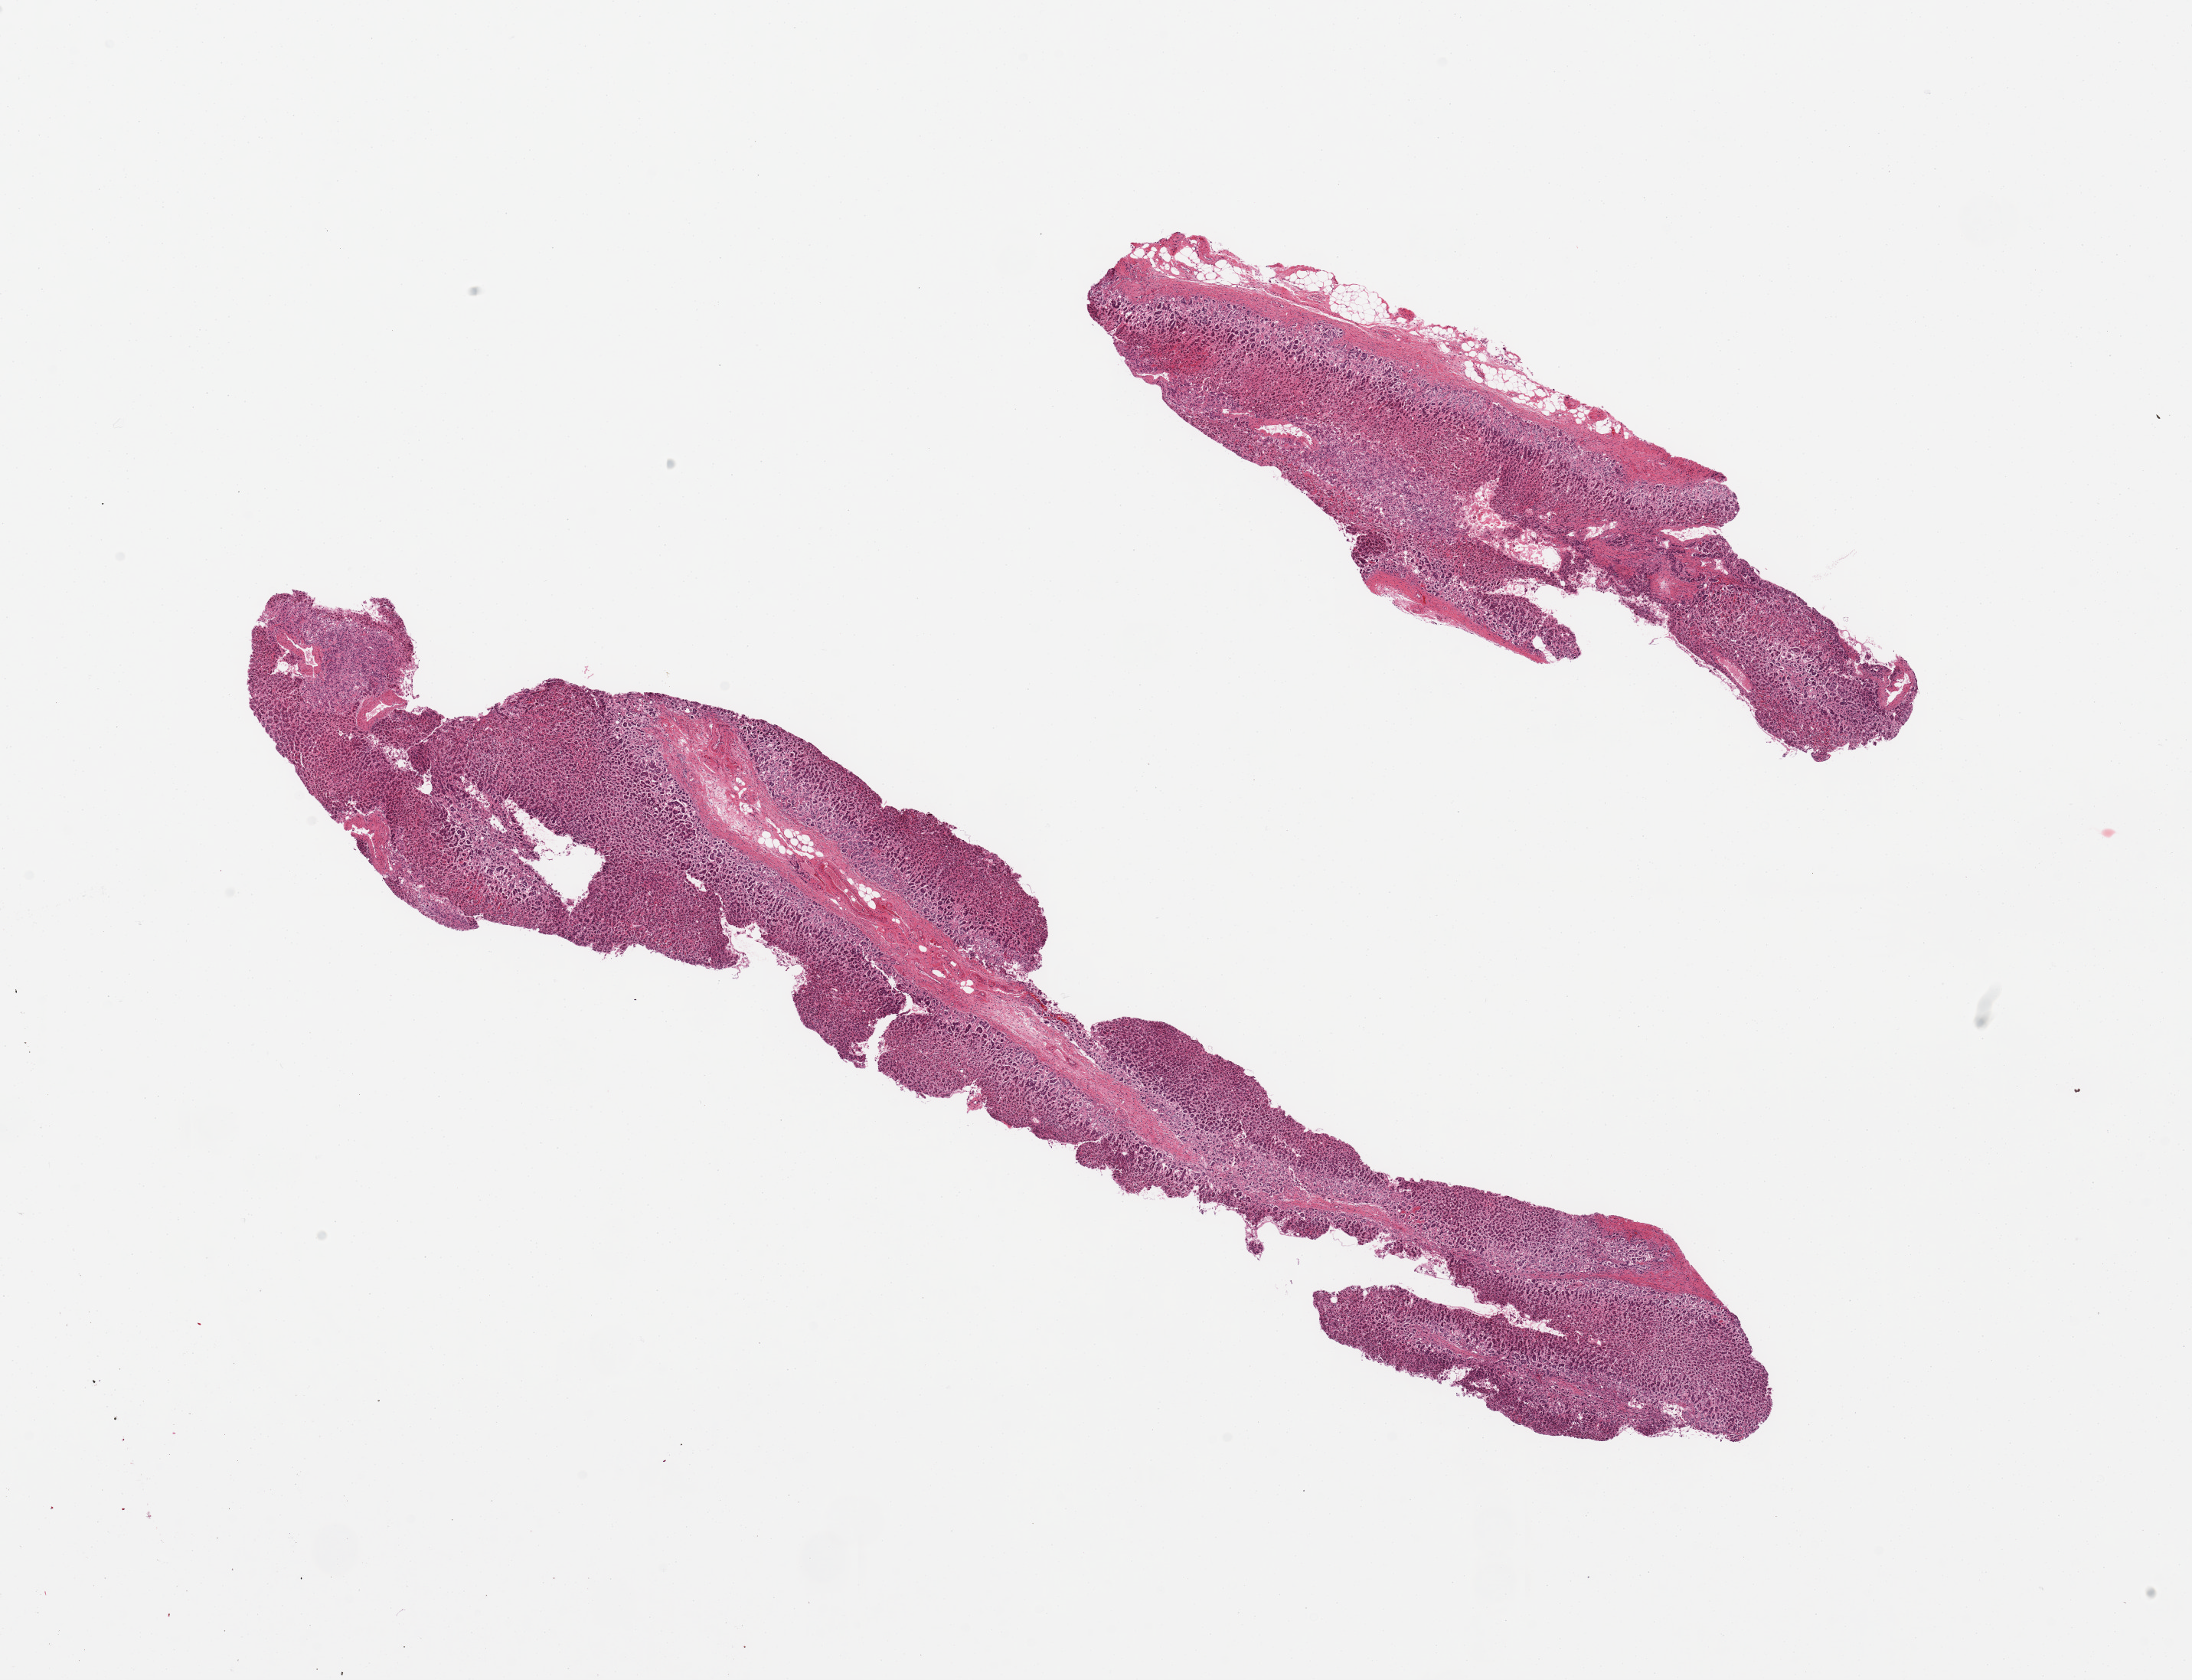
Digitized hematoxylin and eosin (H&E)-stained section, brightfield — shown as a low-resolution overview of the whole scanned area (about 22.6 x 17.4 mm). PAXgene-fixed, paraffin-embedded tissue. Sampled site (target tissue): adrenal gland. Tissue donor sample. Donor sex: female.
Reviewer comment on this tissue sample: 2 pieces.